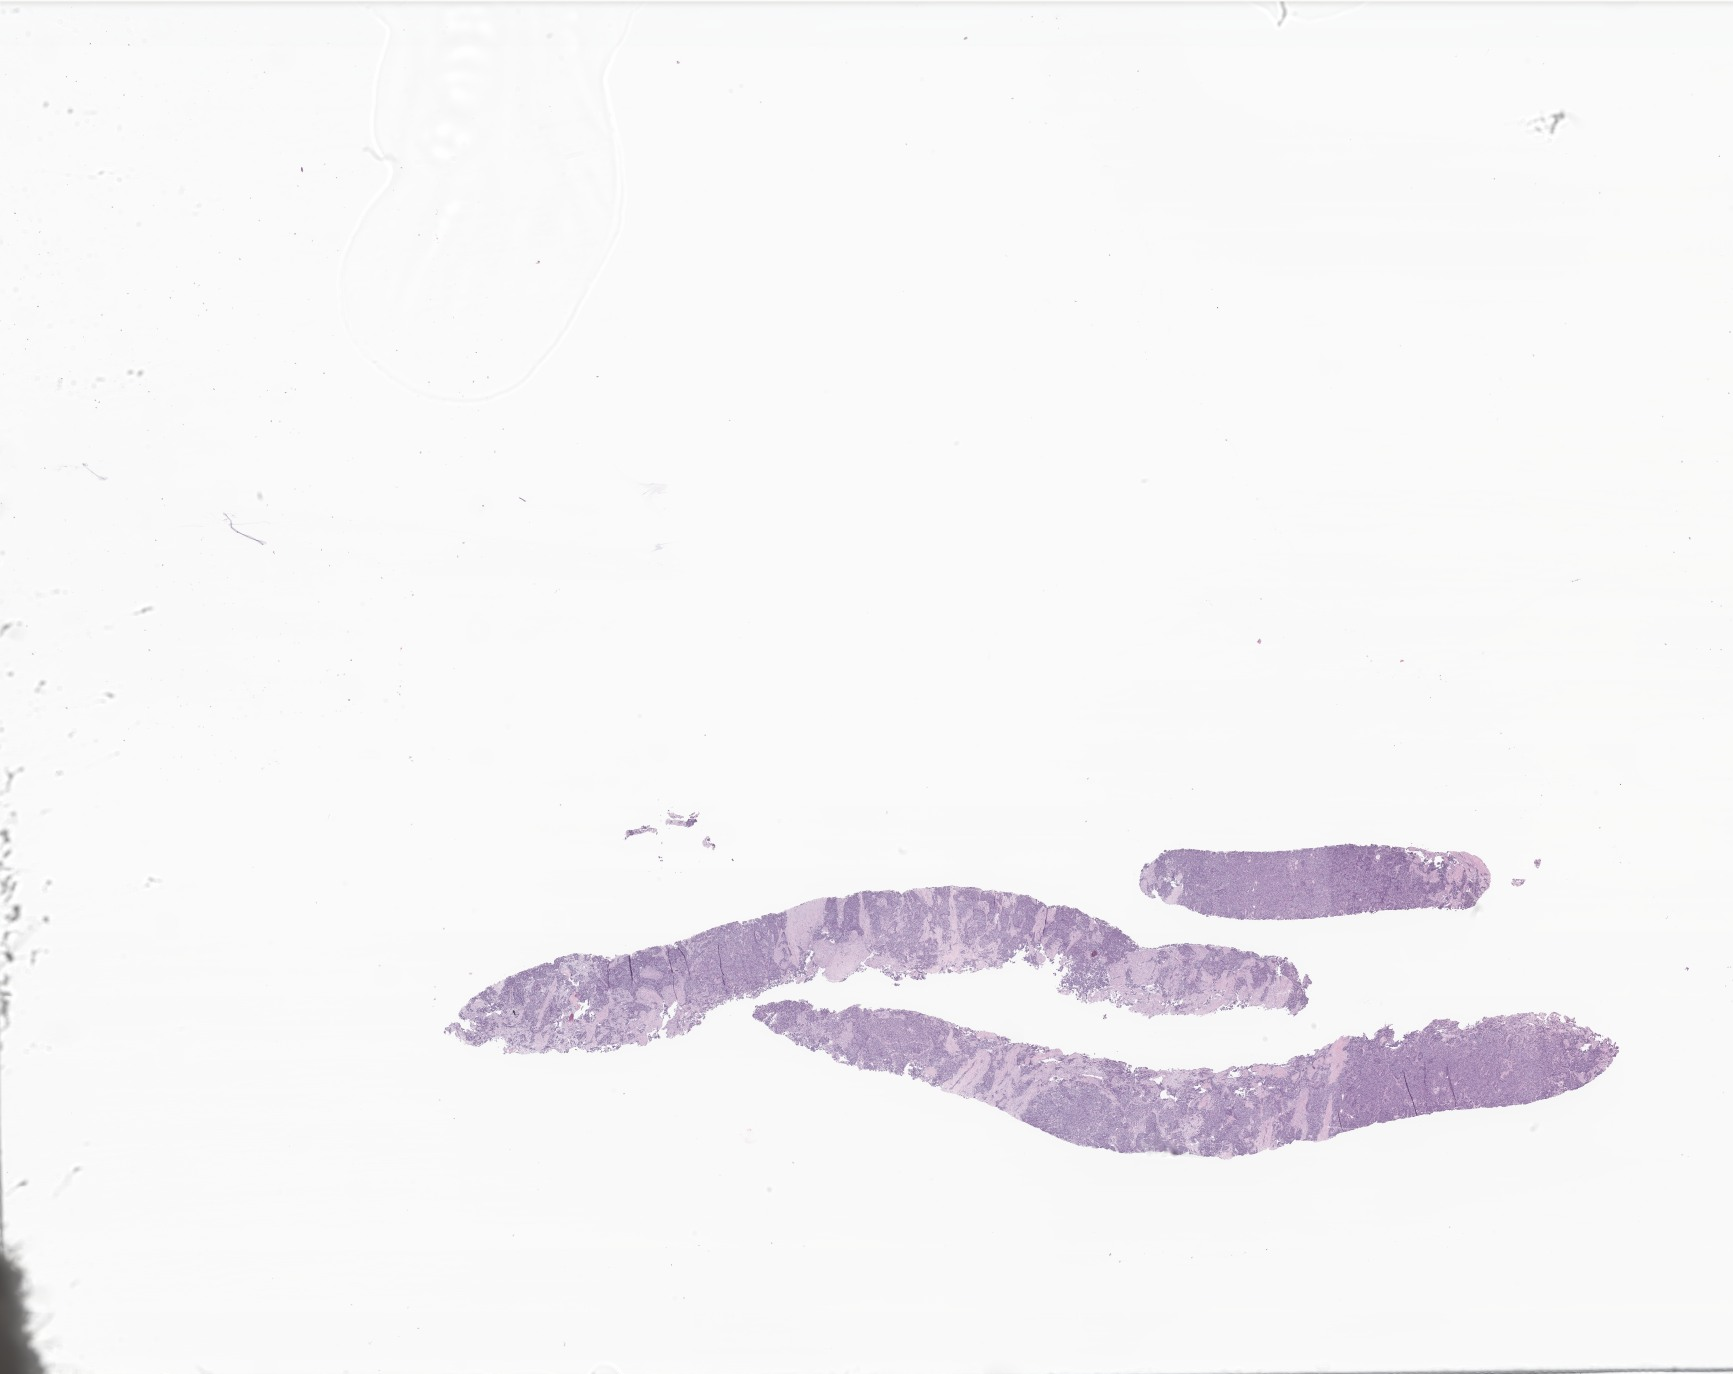
Whole-slide image, hematoxylin and eosin (H&E) stain of tumor tissue from the upper lobe of lung, a low-resolution overview of the entire scanned area, about 29.2 x 23.2 mm. Formalin-fixed, paraffin-embedded (FFPE) tissue. Patient: male, age 204 months (17 years).
• tissue or organ of origin (case record): upper lobe, lung
• diagnosis (ICD-O-3 morphology term): Neuroendocrine carcinoma, NOS